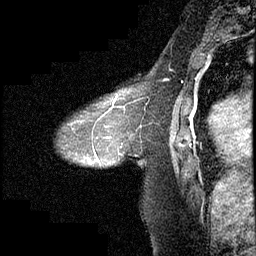
Breast MRI (dynamic contrast-enhanced), one sagittal slice. Position 137 of 232 along the scan axis. Dynamic contrast-enhanced study with each time point stored as its own series, time point 2 of 4 at this slice position (early post-contrast, ordered by acquisition time). 1.5 T. TE 4.2 ms, TR 6.7 ms. 3 mm slice thickness. 256 × 256 image matrix, field of view 200 × 200 mm. Female patient, age 63 years. Case-level facts recorded for this patient, not image findings: setting: breast cancer imaged before/during neoadjuvant chemotherapy; receptor status: triple-negative.
Structures marked on this image (semi-automatic segmentation, software-assisted and operator-edited):
- analysis volume of interest (the breast-tissue region the enhancement analysis was run in; not a lesion): bounding box <57,90,140,168> (left, top, right, bottom; pixels)
- tumour enhancement mask (voxels above the 70 % enhancement threshold inside the analysis volume of interest): <92,93,130,163>